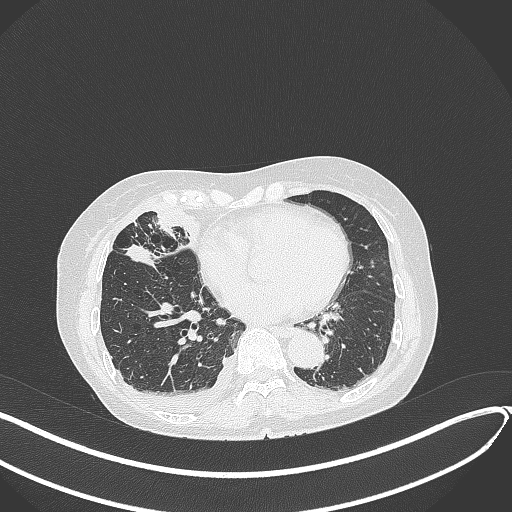
Chest CT, one axial slice. Slice 151 of 418 in the series (ordered by position). Reconstruction kernel B70f. 120 kVp. Lung window (W 1500 / L -600 HU). 1 mm slice thickness. 512 × 512 image matrix, field of view 400 × 400 mm. Patient: female, 75 years. From the clinical record (not read from this slice): clinical TNM (as recorded): T2a N3 M0.
Outlined on this slice (rectangle marked by the reading radiologist):
- lung tumour (recorded histology: adenocarcinoma): bounding box [x1, y1, x2, y2] px = [122, 243, 162, 271]